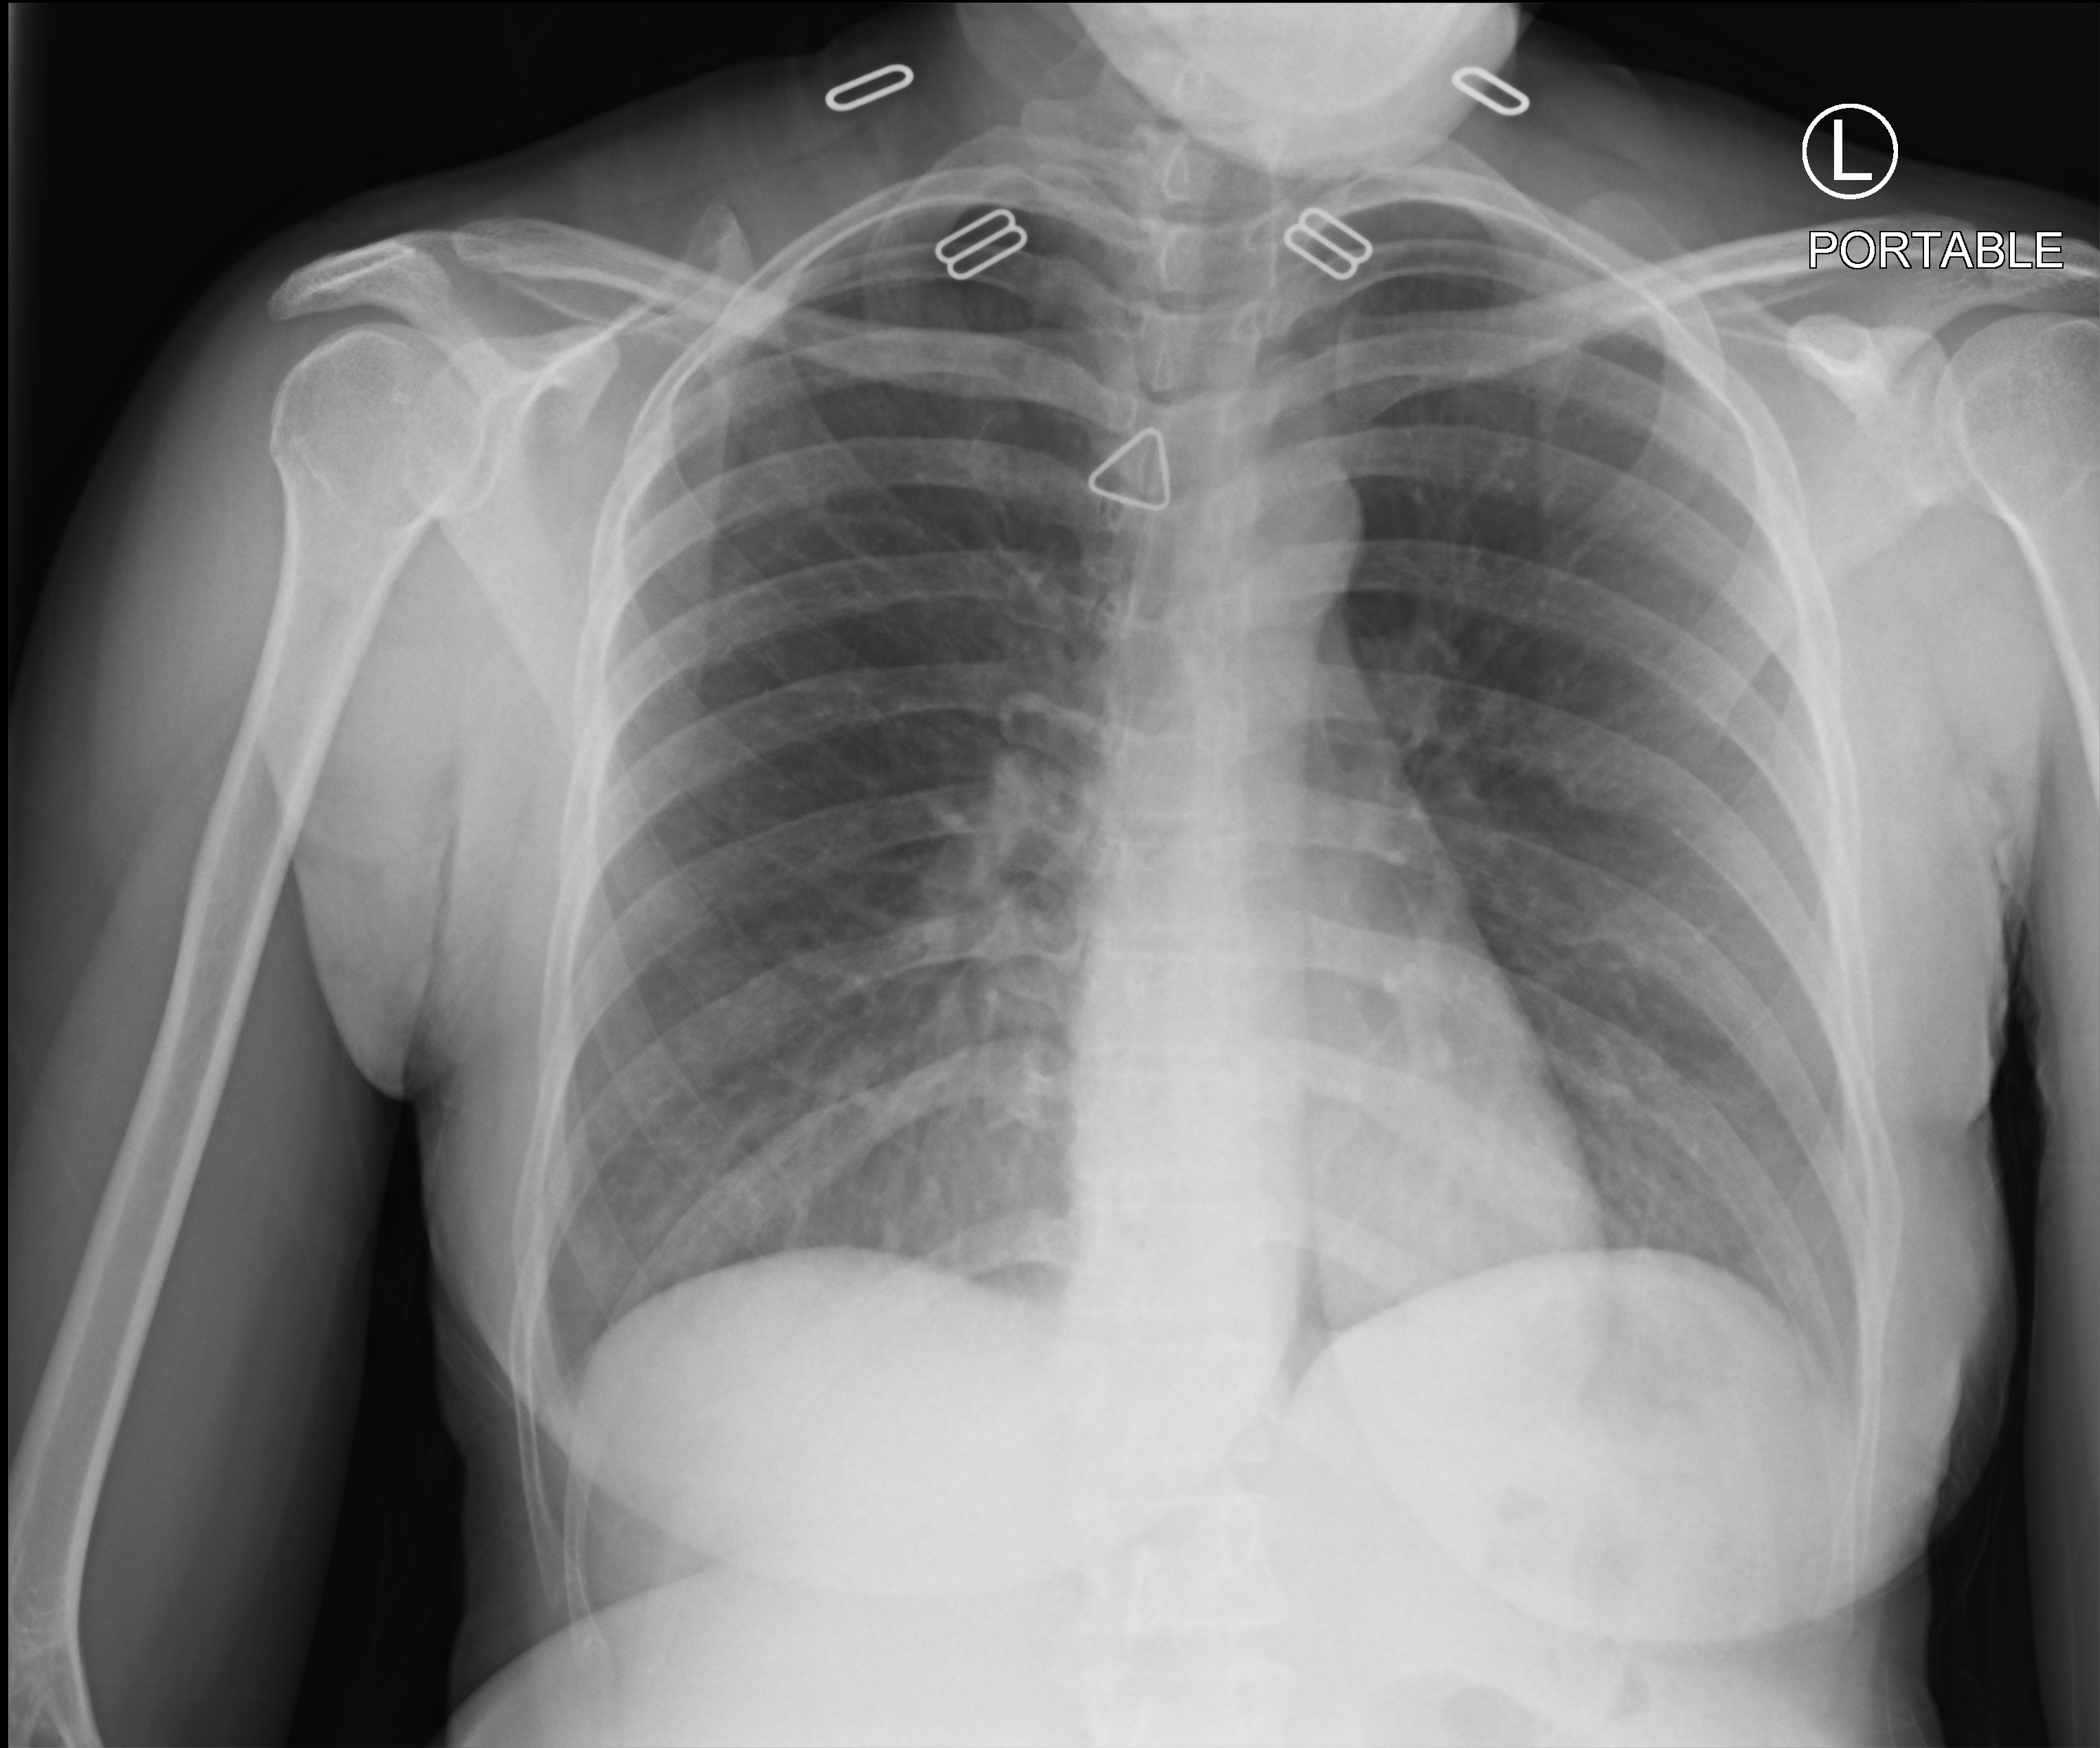
Portable chest radiograph; anteroposterior (AP) projection. Female patient hospitalised with COVID-19, age 18–59 years.
From the hospital-stay record, not from the radiograph (when in the stay this image was taken is not recorded):
- smoking status (admission record): never
- mechanically ventilated during this hospital stay: no